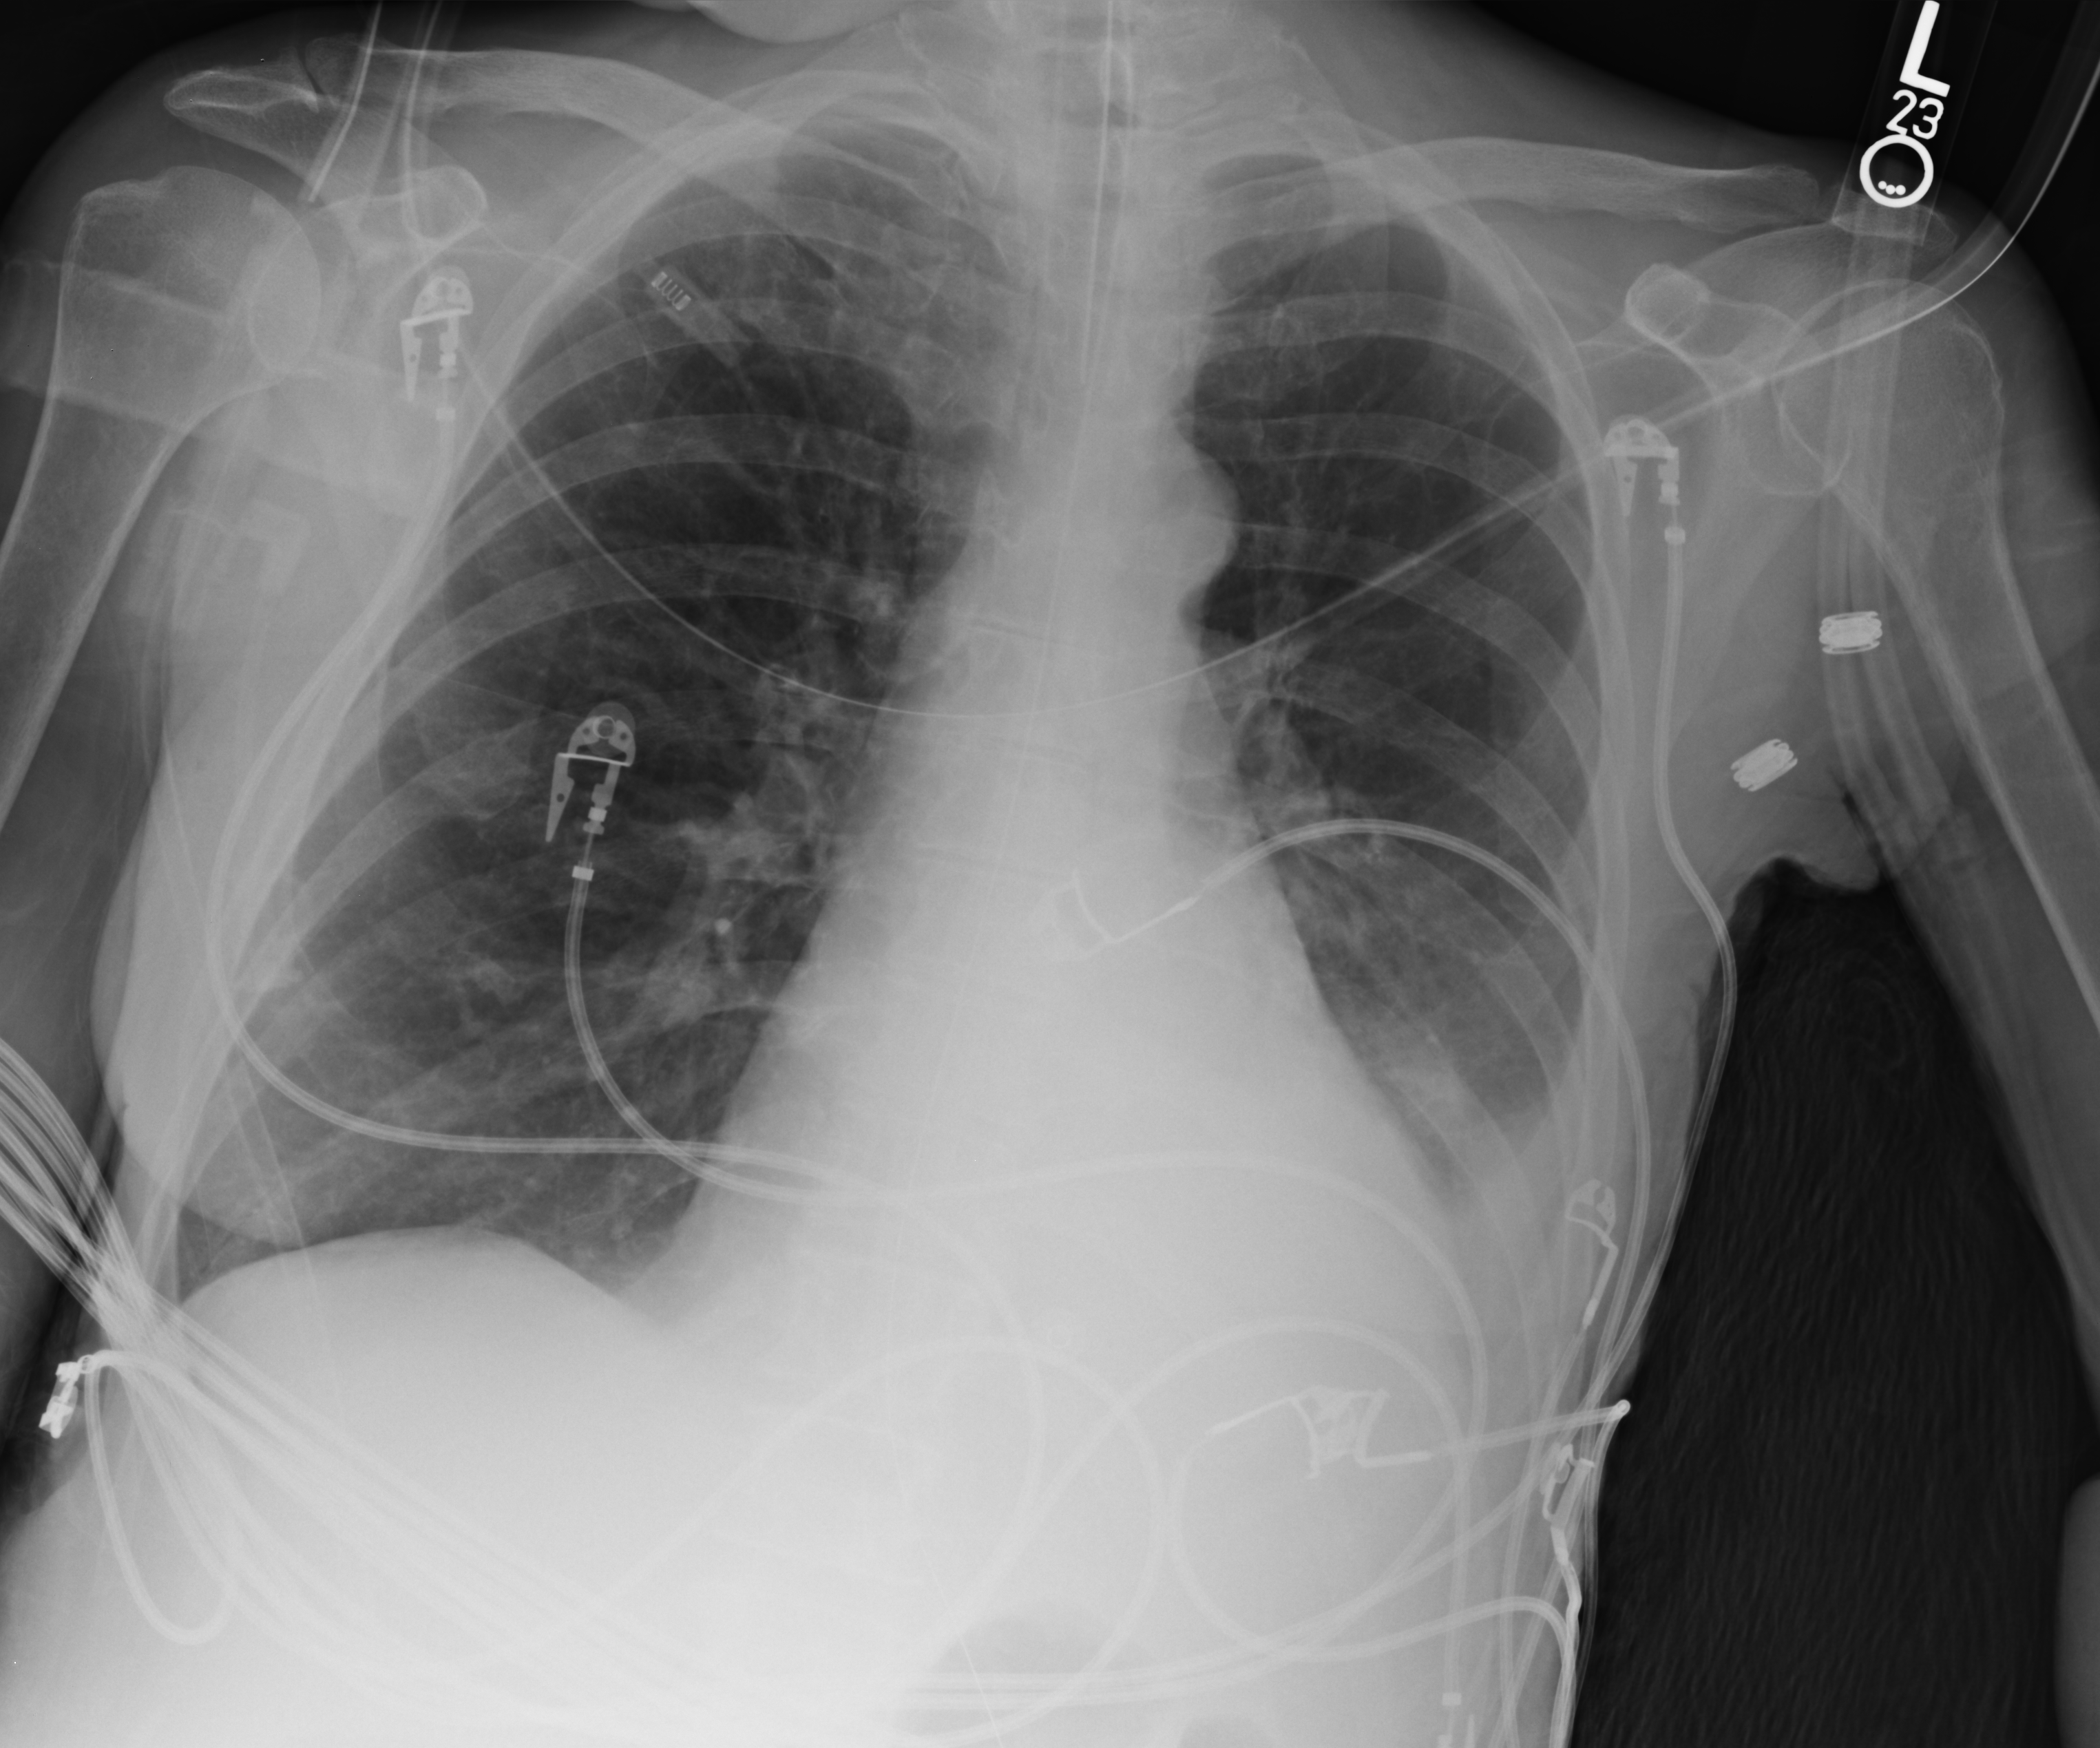
Portable chest radiograph; anteroposterior (AP) projection. Female patient hospitalised with COVID-19, age 60–74 years.
From the hospital-stay record, not from the radiograph (when in the stay this image was taken is not recorded):
- admitted to intensive care during this hospital stay: yes